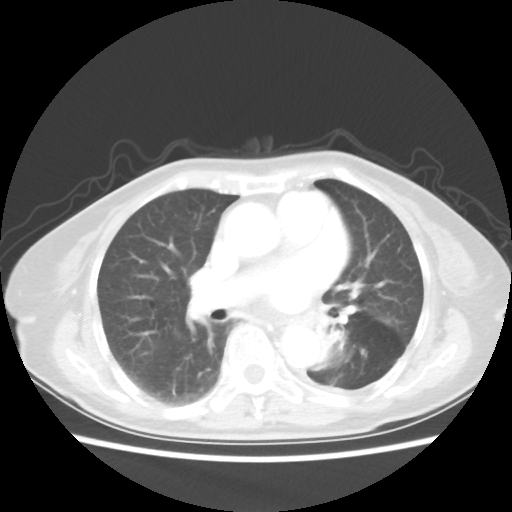
Chest CT, one axial slice. Position 26 of 50 along the scan axis. 80 kVp. Lung window (W 1500 / L -600 HU). 512 × 512 image matrix, field of view 335 × 335 mm. Patient: female, 81 years. From the clinical record (not read from this slice): clinical TNM (as recorded): T2 N0 M1a.
Outlined on this slice (rectangle marked by the reading radiologist):
- lung tumour (recorded histology: squamous cell carcinoma): bounding box <314,320,346,364> (left, top, right, bottom; pixels)